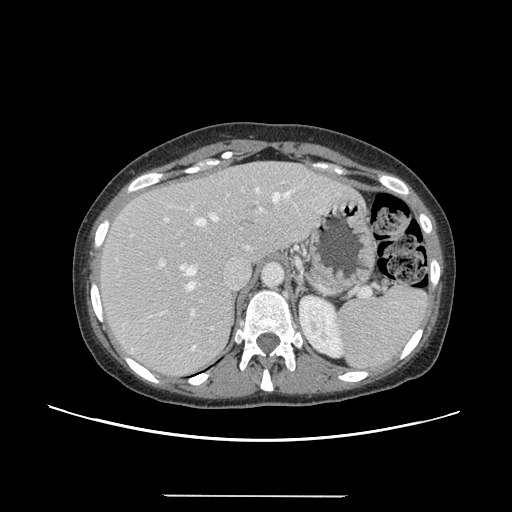
Contrast-enhanced abdominal CT, one axial slice; position 103 of 144 along the scan axis; 120 kVp; intravenous contrast given; soft-tissue window (W 400 / L 40 HU); 2.5 mm slice thickness; 512 × 512 image matrix, field of view 380 × 380 mm. Female patient, age 53 years. From the clinical record (not read from this slice): diagnosis: colorectal cancer liver metastases, imaged before liver resection; multiple liver metastases: yes; largest metastasis: 1.1 cm; disease in both lobes: no.
Outlined on this slice (outlined manually by an expert reader):
- hepatic veins: bounding box [x1, y1, x2, y2] px = [180, 188, 290, 290]
- liver: [99, 162, 358, 376]
- planned liver remnant (the part of the liver to remain after resection): [99, 162, 302, 301]
- portal vein (with intrahepatic branches): [159, 181, 284, 317]